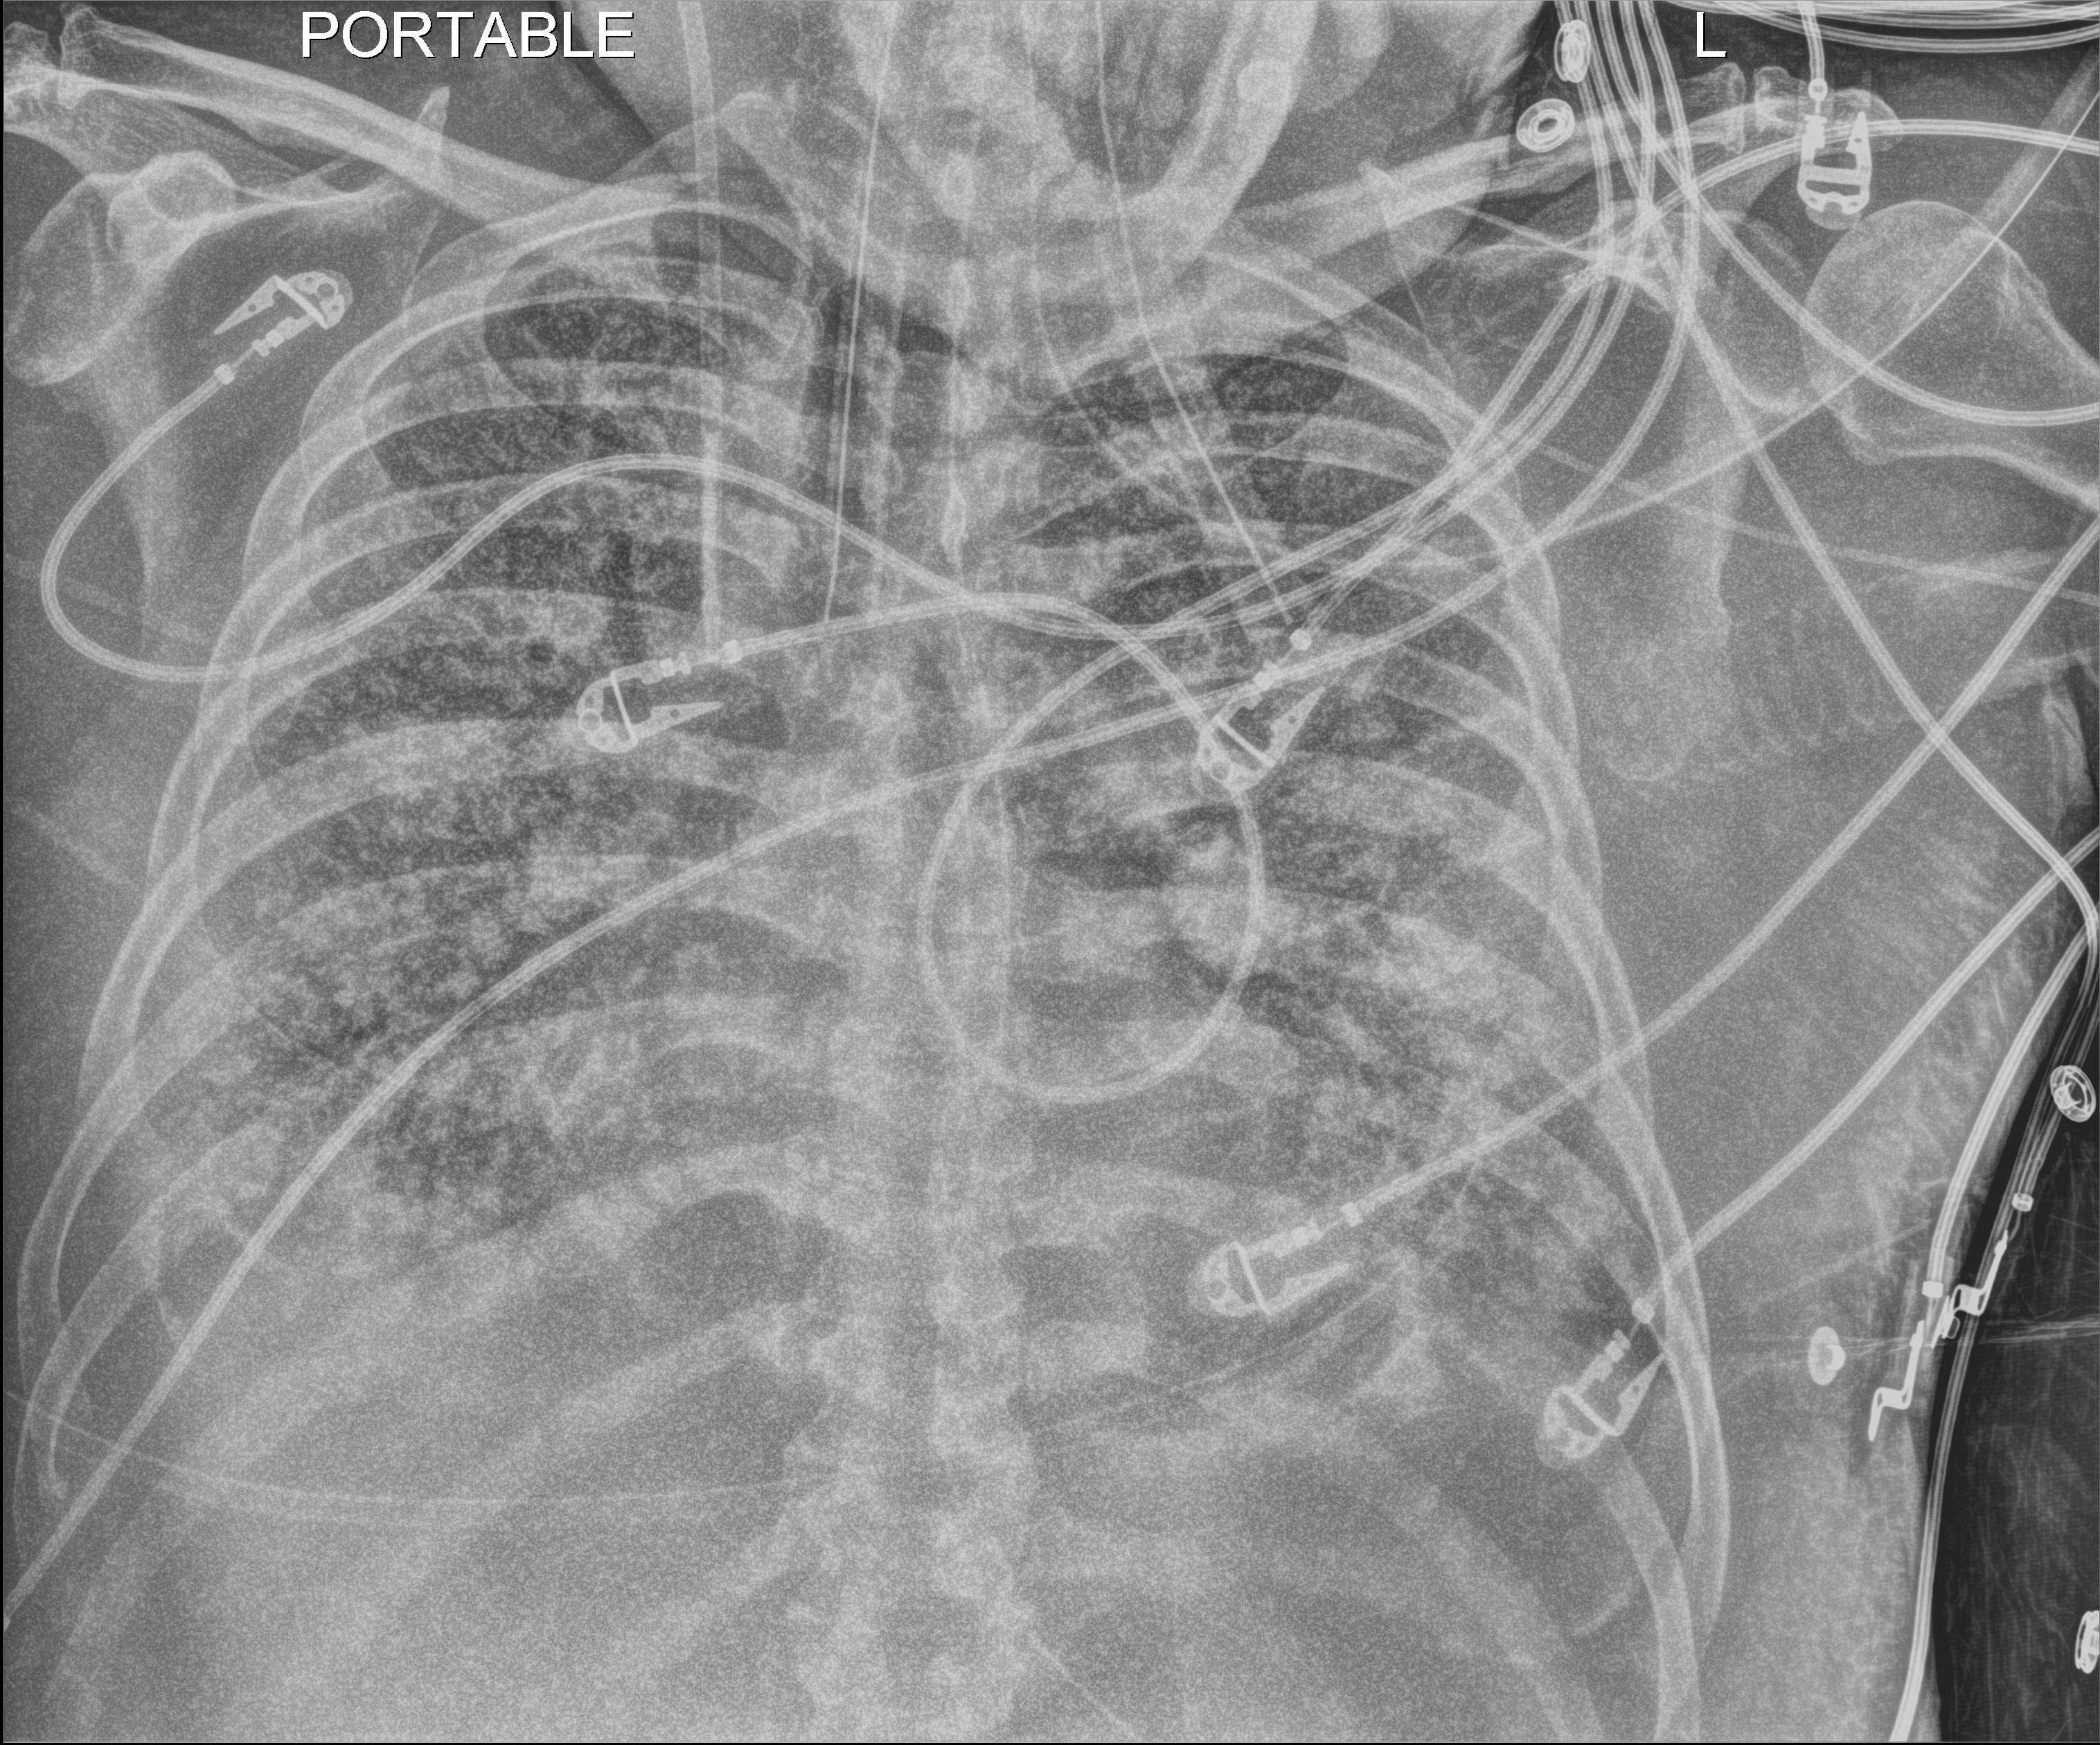
Bedside chest radiograph (digital radiography), anteroposterior (AP) projection. Male patient hospitalised with COVID-19, age 60–74 years.
Admission-level facts for this patient (not findings on this image; timing relative to this image not recorded): hypertension (admission record): yes.